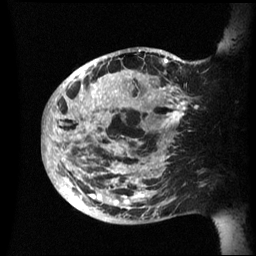
Breast MRI (dynamic contrast-enhanced), one sagittal slice. Position 19 of 60 along the scan axis. Dynamic contrast-enhanced series, image 2 of 3 at this slice position (ordered by acquisition). 1.5 T. TE 4.2 ms, TR 8.4 ms. 2.4 mm slice thickness. 256 × 256 image matrix, field of view 230 × 230 mm. Patient: female, 48 years.
Annotated regions visible in this slice (semi-automatically segmented with operator editing):
- analysis volume of interest (the breast-tissue region the enhancement analysis was run in; not a lesion): bounding box <43,47,202,224> (left, top, right, bottom; pixels)
- tumour enhancement mask (voxels above the 70 % enhancement threshold inside the analysis volume of interest): <43,49,194,209>